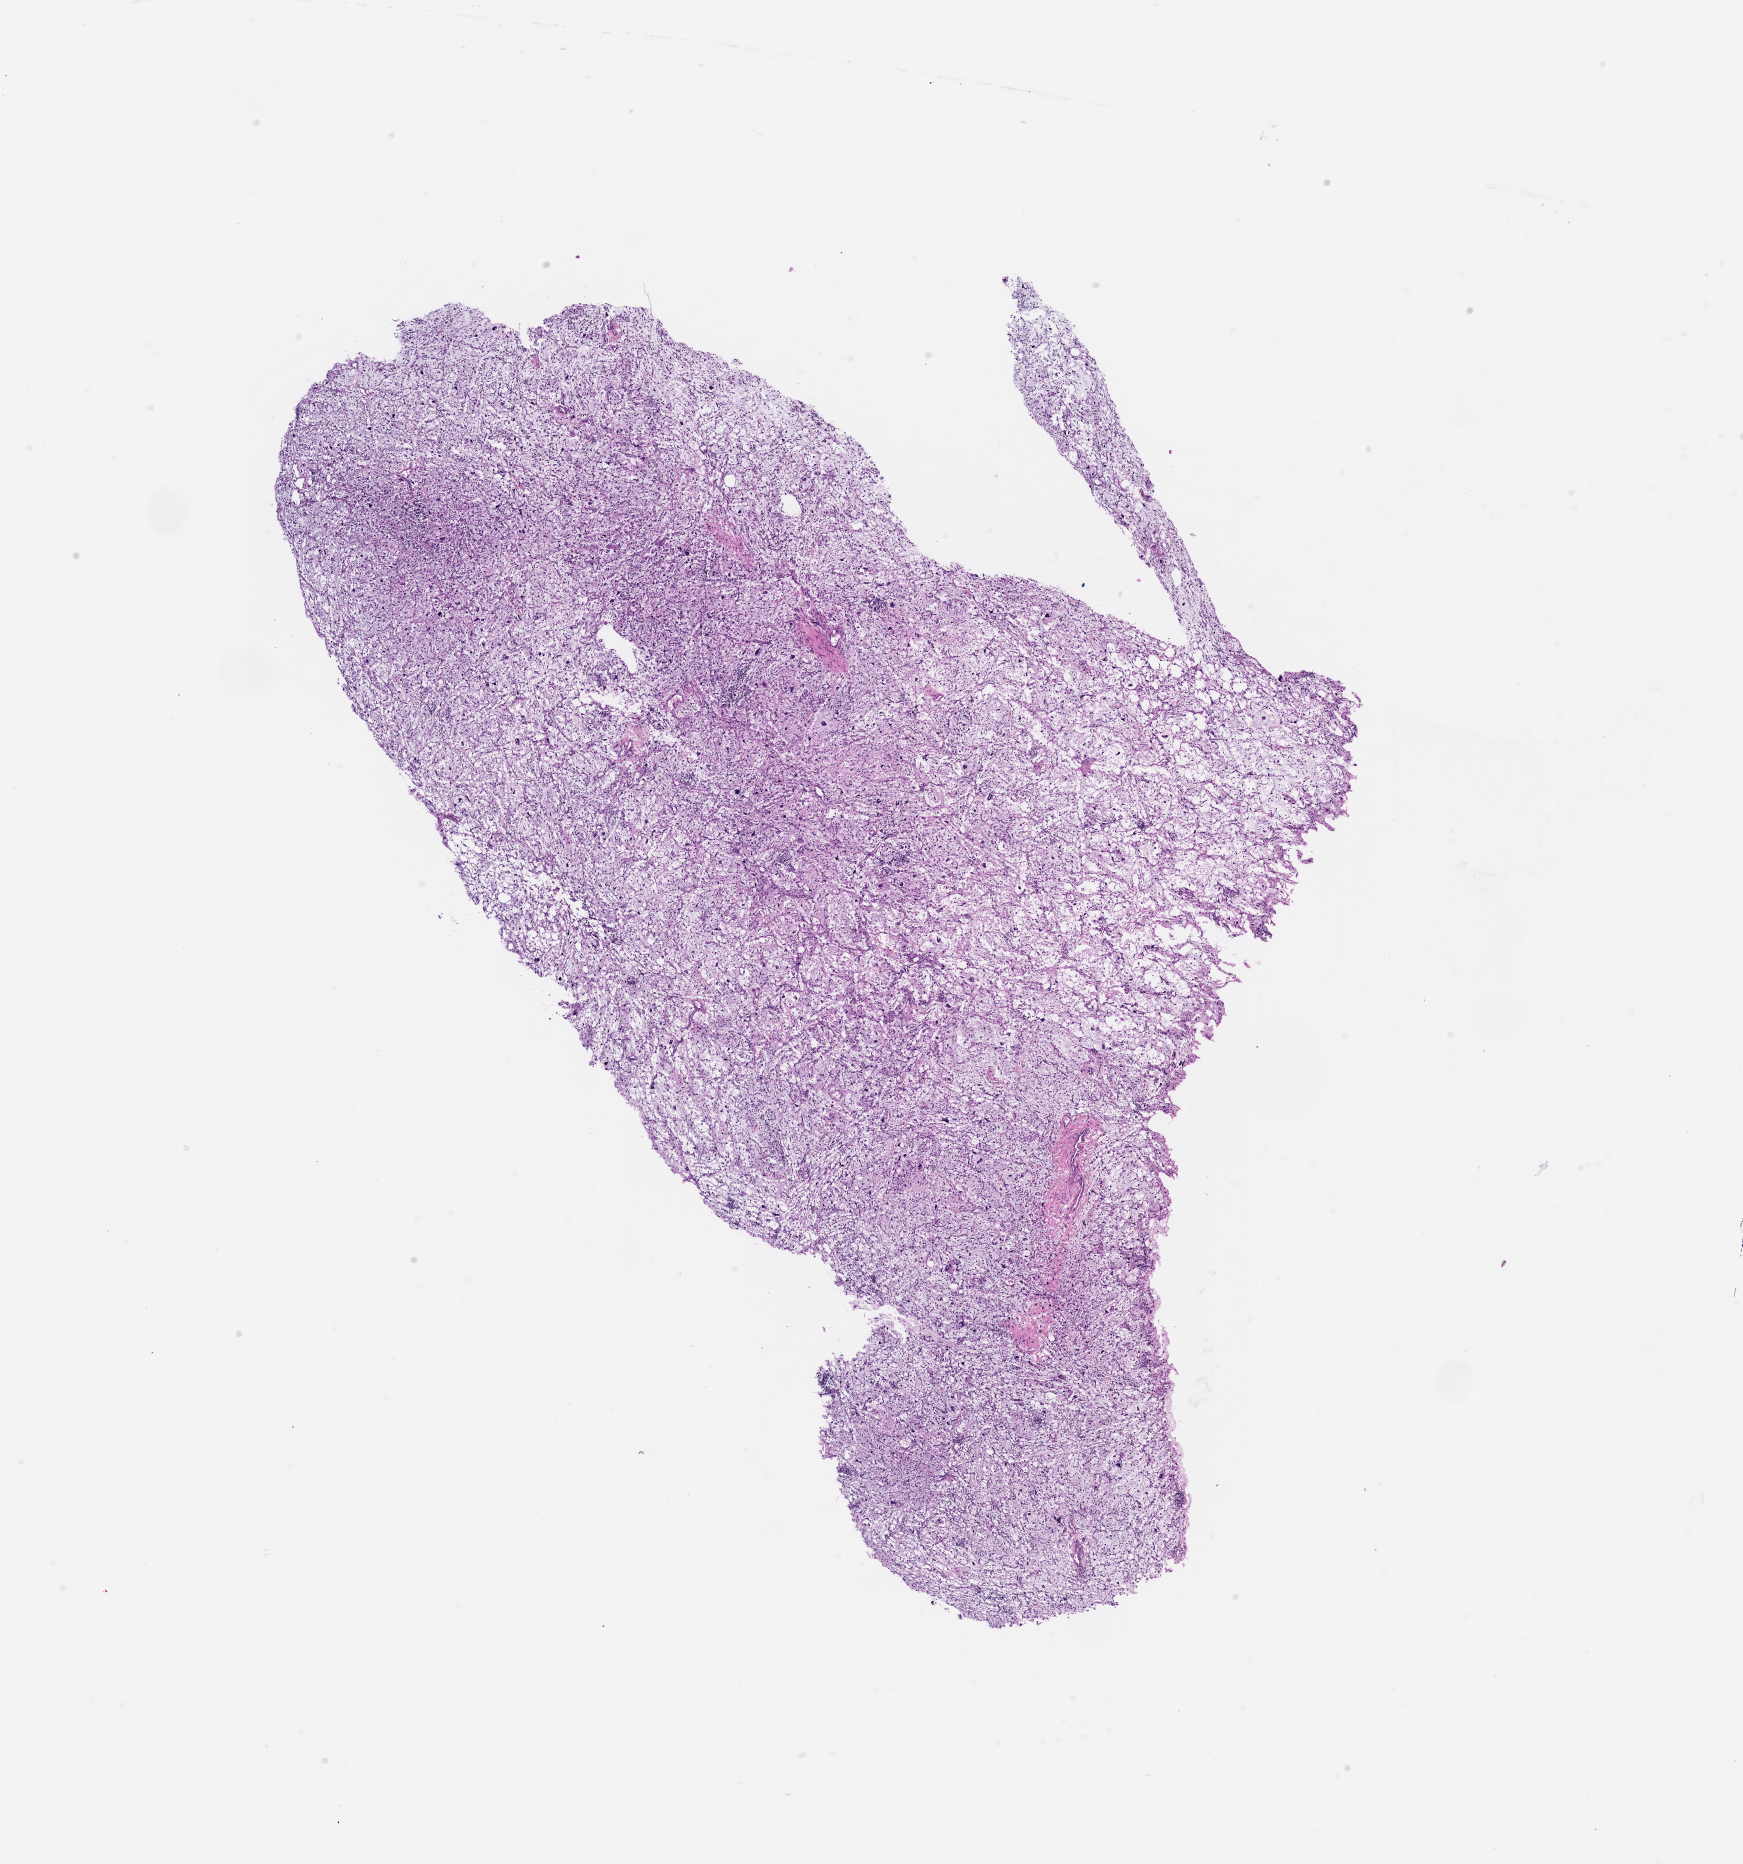
H&E whole-slide image, low-resolution overview of the scanned area, about 14.0 x 15.0 mm (acquisition: 20x scan).
Patient diagnosis (cohort enrolment): sarcoma (site not recorded at cohort level).